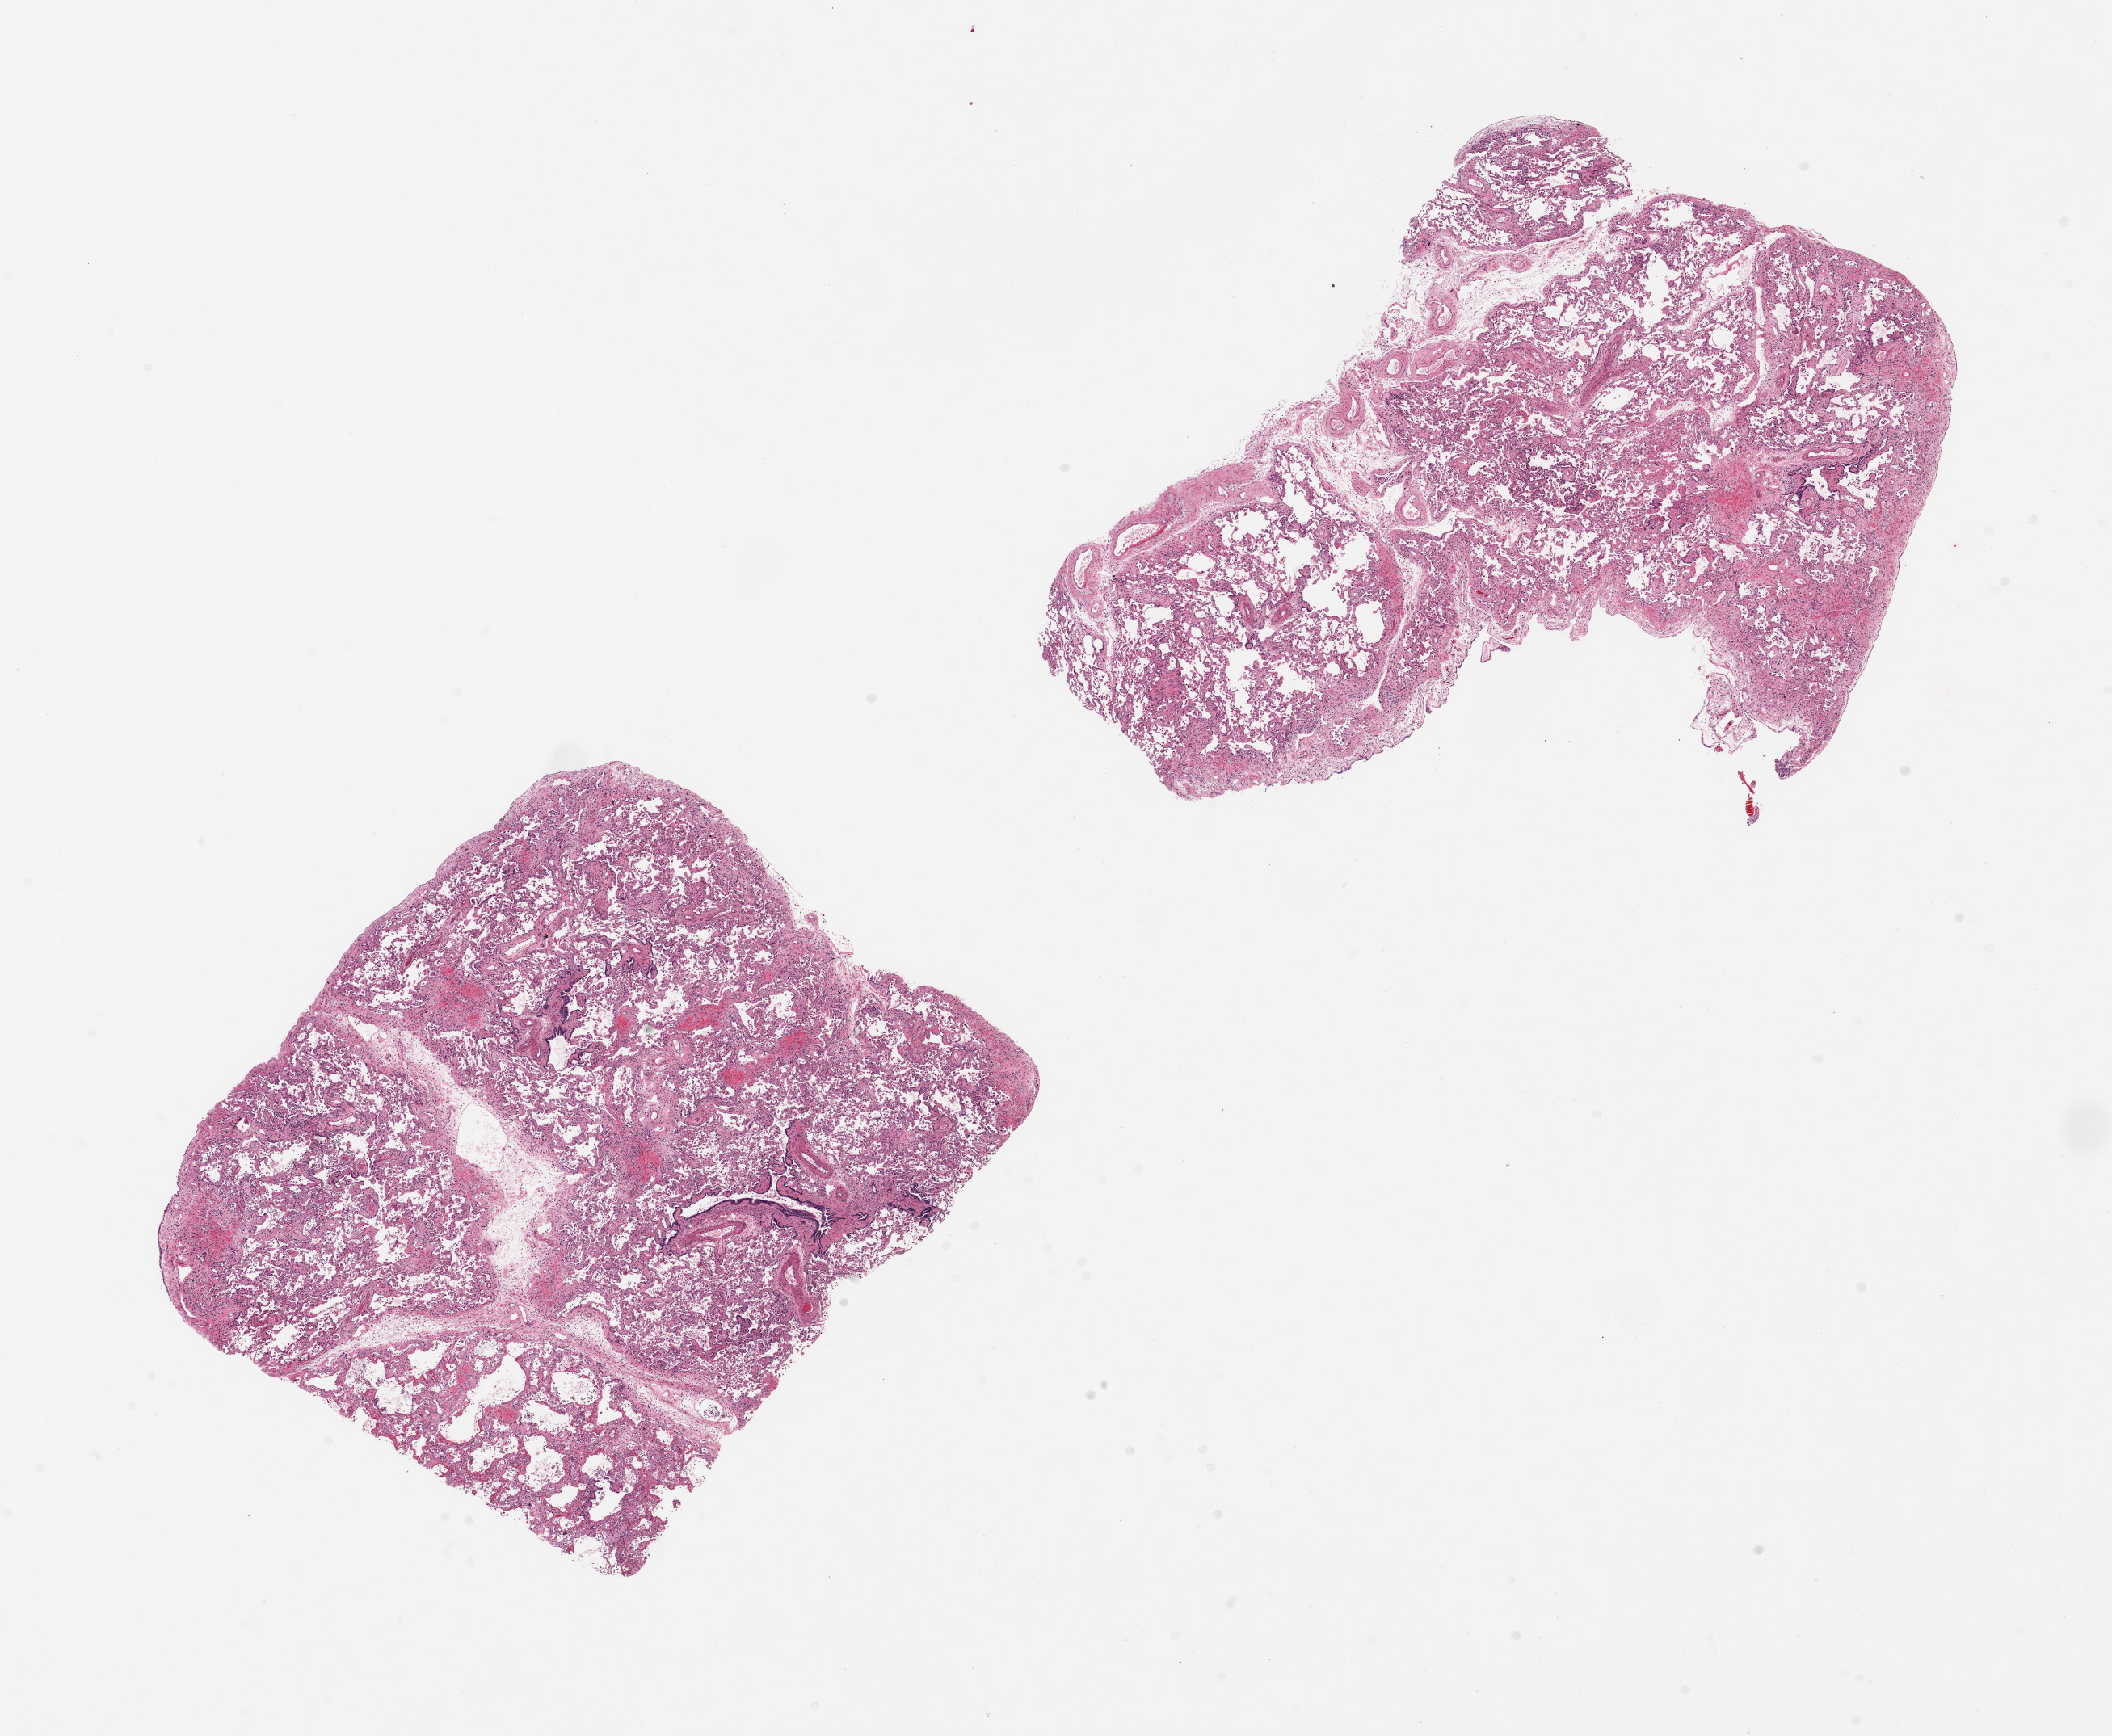
Haematoxylin and eosin whole-slide image — whole scanned area (about 20.7 x 17.0 mm) shown as a low-resolution overview; PAXgene-fixed, paraffin-embedded tissue; target tissue: lung; donor tissue sample.
* reviewer comment on this tissue sample: 2 pieces; patchy pneumonia and fibrosis